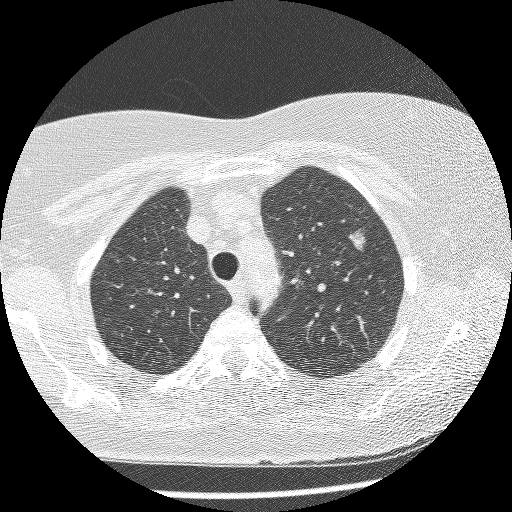
Low-dose screening chest CT, axial slice, baseline annual screen, lung window (W 1500 / L -600 HU), 1.25 mm slice thickness, lung (sharp) reconstruction kernel (BONE). Female participant, aged 61 years at enrolment.
Lesion marked by an expert reader, bounding box [x1, y1, x2, y2] px = [329, 219, 382, 267]. The screening reader recorded 4 non-calcified nodules or masses ≥4 mm on this exam; which of them this box marks is not recorded. Lung cancer was diagnosed 111 days after this screen: bronchiolo-alveolar adenocarcinoma, NOS, left upper lobe, stage IV (AJCC 6th edition), 10 mm at pathology.